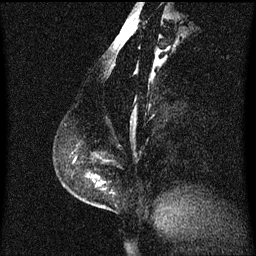
Breast MRI (dynamic contrast-enhanced), one sagittal slice. Position 23 of 60 along the scan axis. Dynamic contrast-enhanced series, image 2 of 3 at this slice position (ordered by acquisition). 1.5 T. TE 4.2 ms, TR 8.4 ms. 2 mm slice thickness. 256 × 256 image matrix, field of view 200 × 200 mm. Female patient, age 40 years. From the clinical record (not read from this slice): setting: breast cancer imaged before/during neoadjuvant chemotherapy; receptor status: triple-negative.
Annotated regions visible in this slice (semi-automatically segmented with operator editing):
- analysis volume of interest (the breast-tissue region the enhancement analysis was run in; not a lesion): bounding box <62,152,113,211> (left, top, right, bottom; pixels)
- tumour enhancement mask (voxels above the 70 % enhancement threshold inside the analysis volume of interest): <94,180,103,185>